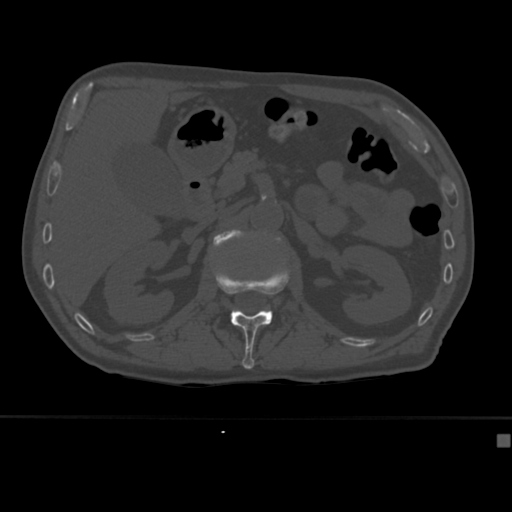
CT including the spine, one axial slice; position 165 of 430 along the scan axis; reconstruction kernel Br40s; bone window (W 1800 / L 400 HU); 1.5 mm slice thickness; 512 × 512 image matrix. Male patient, age 64 years. Case-level facts recorded for this patient, not image findings: primary cancer: uterus.
Annotated regions visible in this slice (semi-automatically segmented with operator editing):
- L1 vertebra: box from (x=214, y=263) to (x=289, y=369) px
- L2 vertebra: (x=213, y=229)–(x=281, y=249)